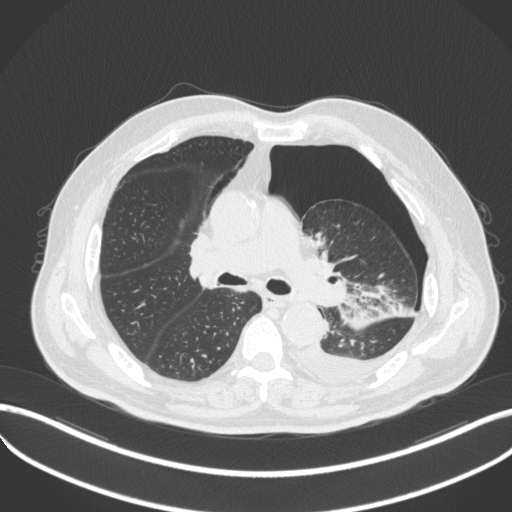
Chest CT, one axial slice. Position 311 of 466 along the scan axis. Reconstruction kernel B31f. Lung window (W 1500 / L -600 HU). 1 mm slice thickness. 512 × 512 image matrix, field of view 400 × 400 mm. Male patient, age 76 years. Case-level facts recorded for this patient, not image findings: clinical TNM (as recorded): T3 N0 M1b.
Outlined on this slice (rectangle marked by the reading radiologist):
- lung tumour (recorded histology: adenocarcinoma): bounding box [x1, y1, x2, y2] px = [335, 280, 390, 329]